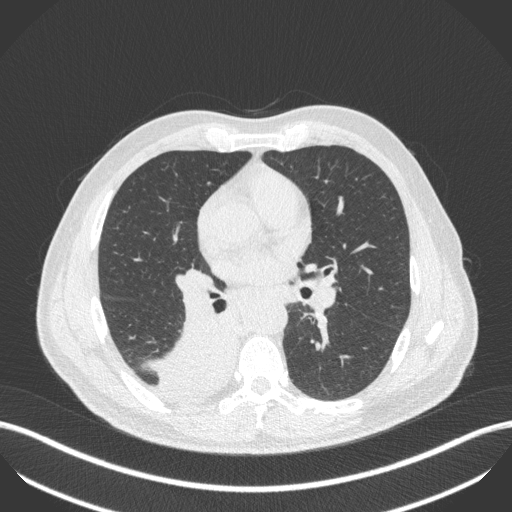
Chest CT, one axial slice. Position 253 of 451 along the scan axis. Reconstruction kernel B31f. Lung window (W 1500 / L -600 HU). 512 × 512 image matrix, field of view 400 × 400 mm. Male patient, age 61 years. Case-level facts recorded for this patient, not image findings: clinical TNM (as recorded): T1 N0 M0.
Structures marked on this image (rectangle marked by the reading radiologist):
- lung tumour (recorded histology: small cell carcinoma): box from (x=143, y=317) to (x=238, y=402) px